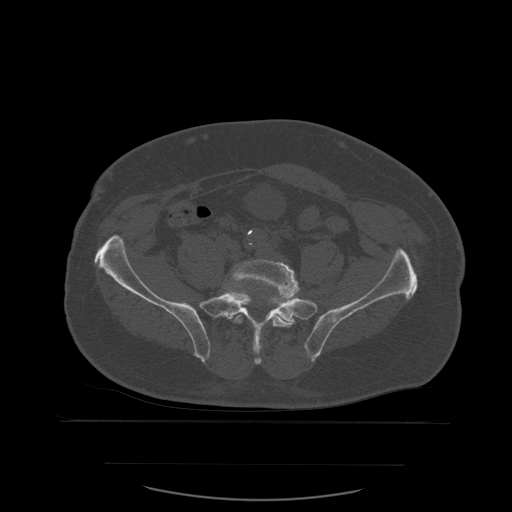
CT including the spine, one axial slice; slice 126 of 590 in the series (ordered by position); bone window (W 1800 / L 400 HU); 1.25 mm slice thickness; 512 × 512 image matrix, field of view 479 × 479 mm. Patient age 71 years. From the clinical record (not read from this slice): primary cancer: lung; vertebrae with lytic lesions (as recorded): T1, T2, L5, S1.
Annotated regions visible in this slice (semi-automatic segmentation, software-assisted and operator-edited):
- L5 vertebra: bounding box <220,260,300,354> (left, top, right, bottom; pixels)